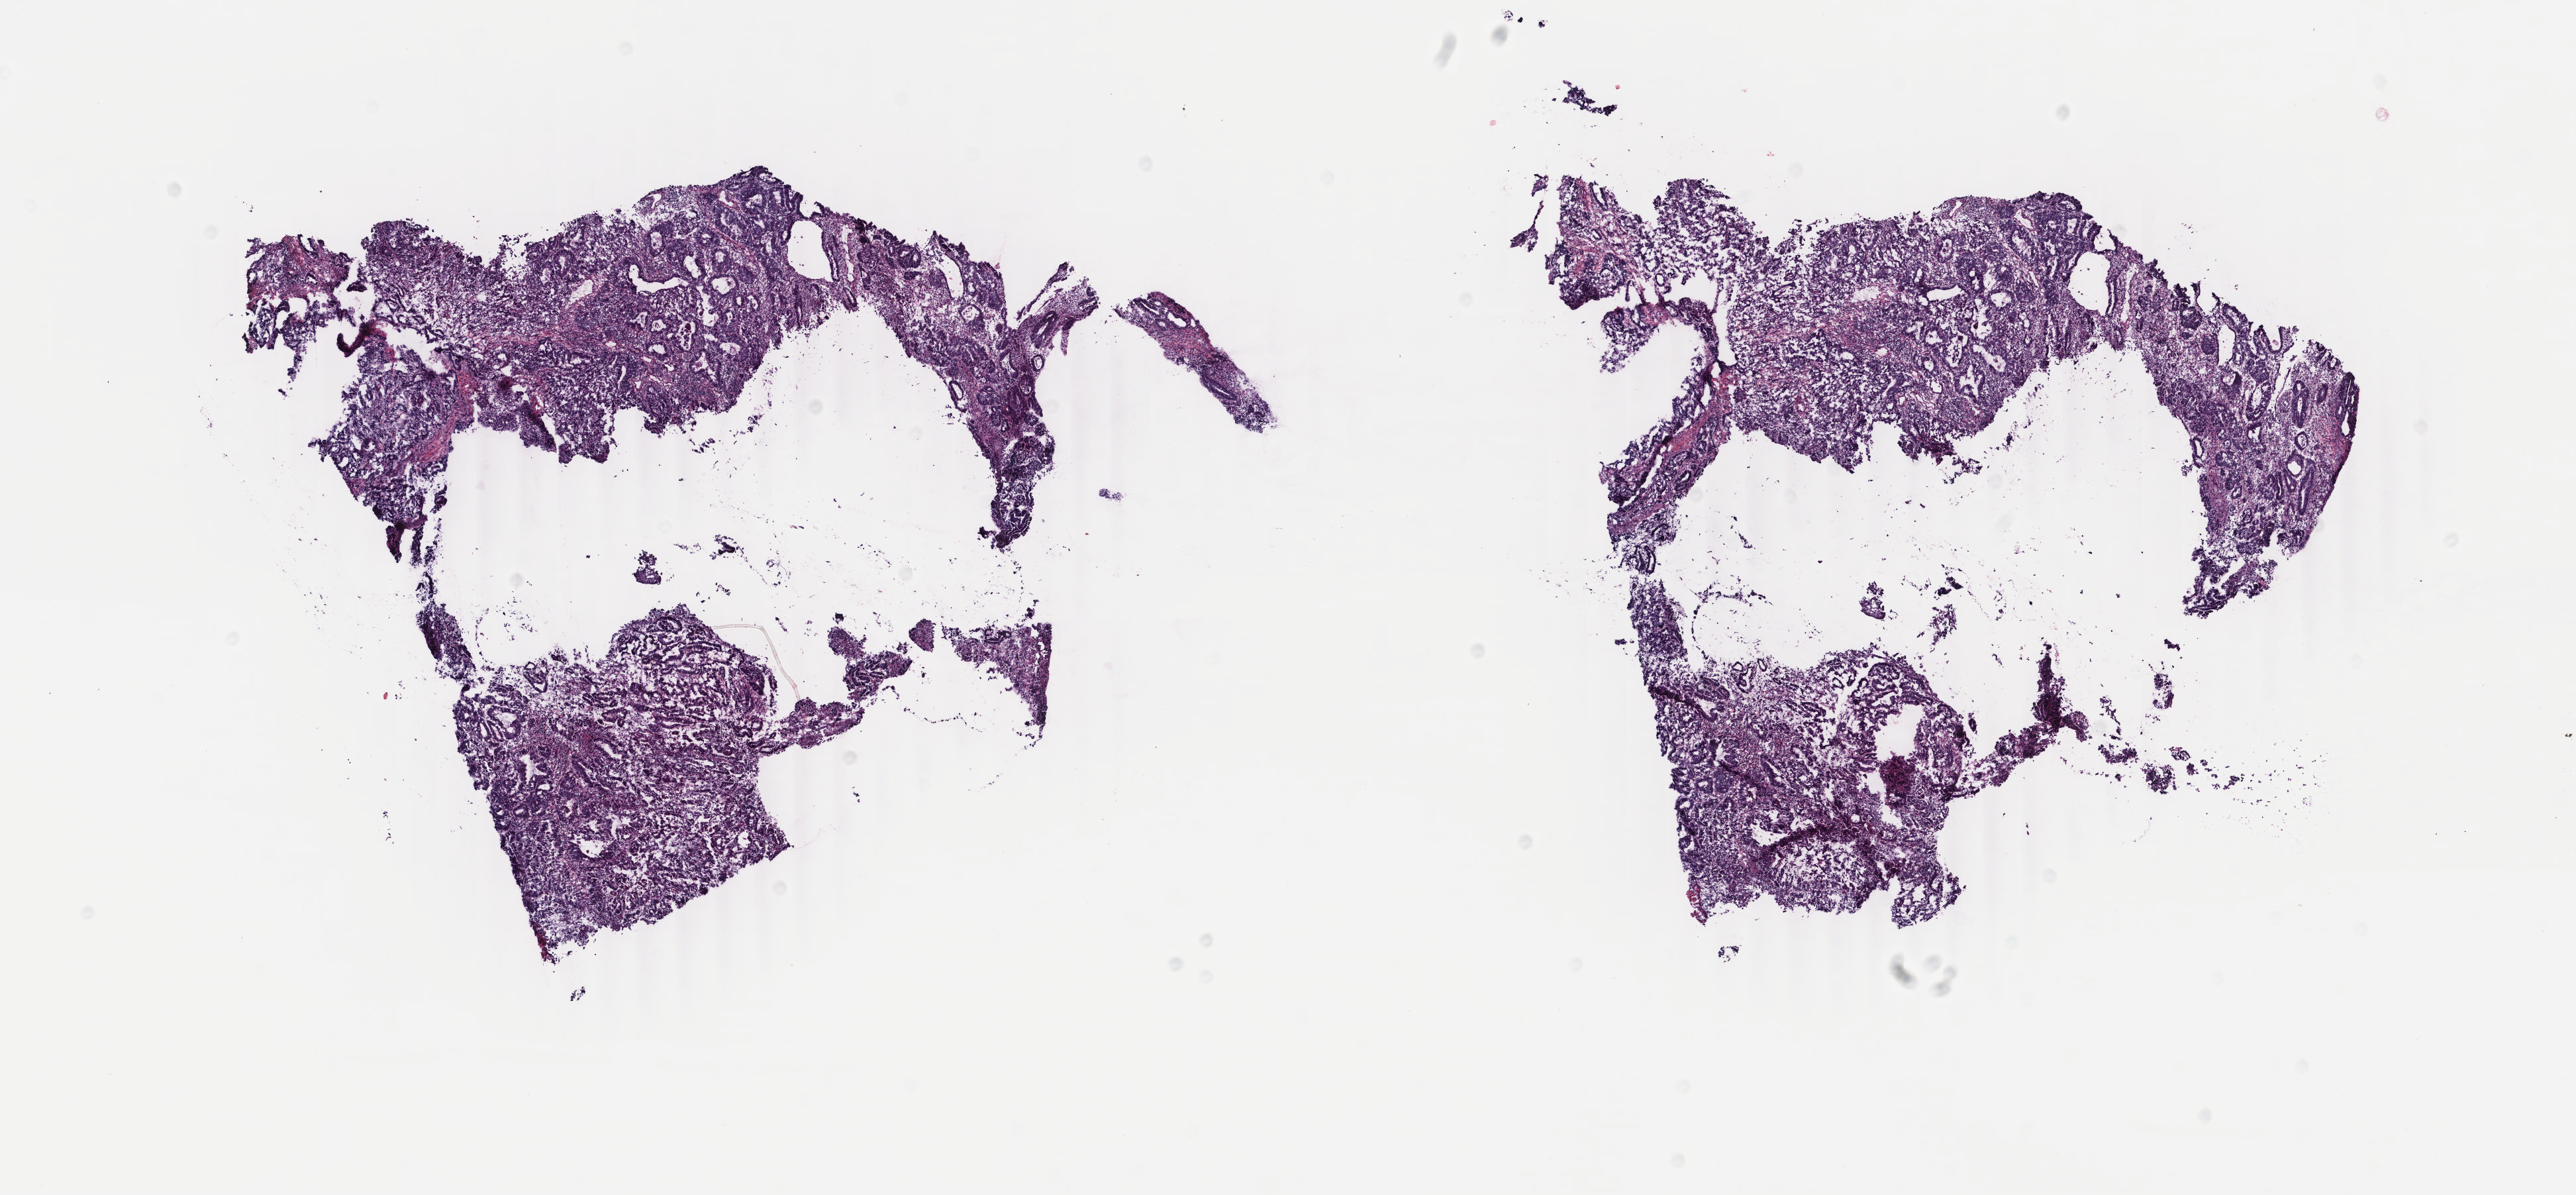
Digitized H&E-stained tissue section (whole slide) — whole scanned area (about 15.5 x 7.2 mm, from a 40x scan) shown as a low-resolution overview. Frozen section from the bottom of the tissue portion. Primary tumour sample from the uterus. Female patient; age at initial diagnosis 58 years.
Pathologic diagnosis: Endometrioid adenocarcinoma, NOS (endometrium).